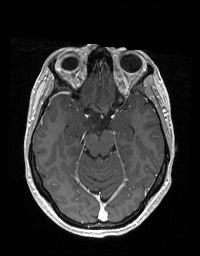
Brain MRI from a brain-tumour surgery series, one axial slice; slice 118 of 192 in the series (ordered by position); T1-weighted post-contrast; 200 × 256 image matrix, field of view 195 × 250 mm. From the clinical record (not read from this slice): histopathology: Glioblastoma; WHO grade: 2; IDH mutation: no; tumour location: Right Skull Base Temporal.
Annotated regions visible in this slice (outlined manually by an expert reader):
- tumour: box from (x=73, y=113) to (x=102, y=138) px